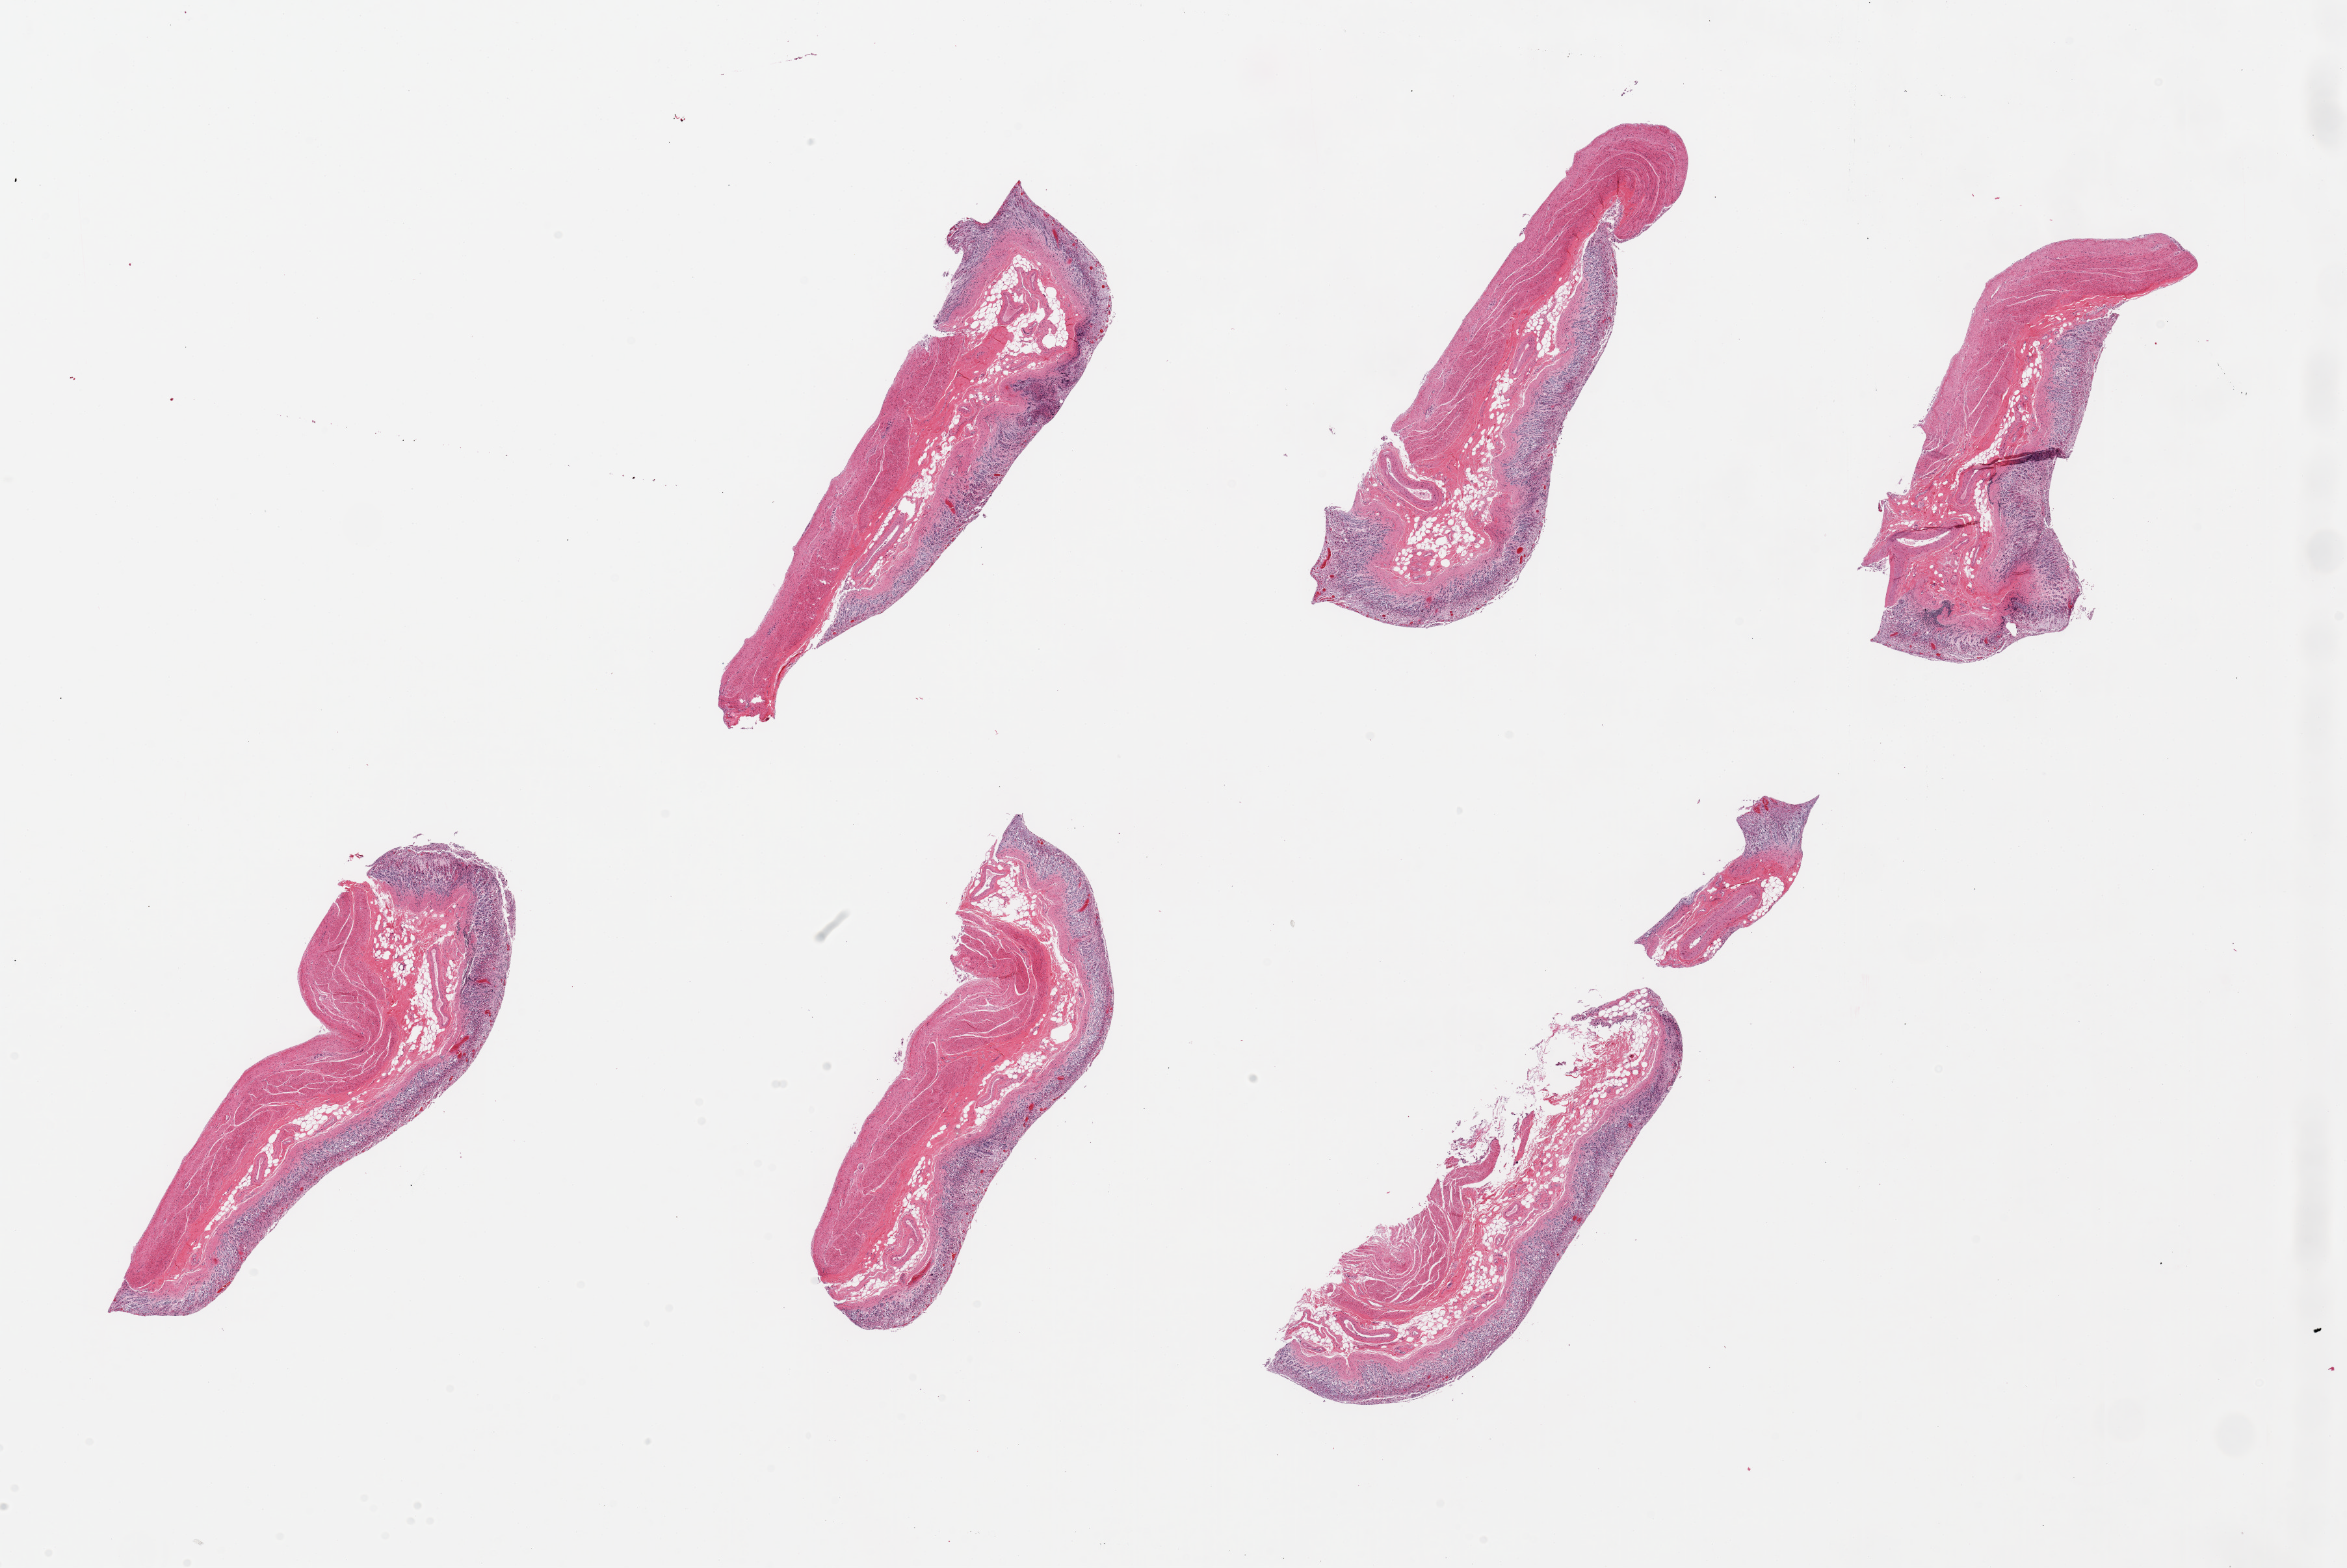
Haematoxylin and eosin whole-slide image, brightfield — a low-resolution overview of the entire scanned area, about 28.5 x 19.1 mm. PAXgene-fixed paraffin-embedded (PFPE) section. Sampled site (target tissue): stomach. Donor tissue sample. Male donor.
Reviewer comment on this tissue sample: 6 pieces, up to 9.5x2mm; Glands = 3; muscle = 2.